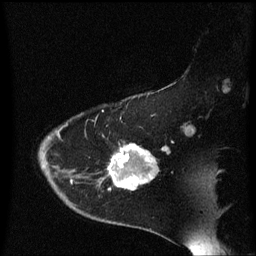
Breast MRI (dynamic contrast-enhanced), one sagittal slice. Slice 46 of 60 in the series (ordered by position). Dynamic contrast-enhanced series, image 2 of 3 at this slice position (ordered by acquisition). 1.5 T. TE 4.2 ms, TR 8.4 ms. 2 mm slice thickness. 256 × 256 image matrix. Patient: female, 54 years. Case-level facts recorded for this patient, not image findings: setting: breast cancer imaged before/during neoadjuvant chemotherapy; receptor status: HR-positive, HER2-negative.
Outlined on this slice (semi-automatic segmentation, software-assisted and operator-edited):
- analysis volume of interest (the breast-tissue region the enhancement analysis was run in; not a lesion): bounding box [x1, y1, x2, y2] px = [102, 132, 158, 191]
- tumour enhancement mask (voxels above the 70 % enhancement threshold inside the analysis volume of interest): [110, 144, 157, 191]